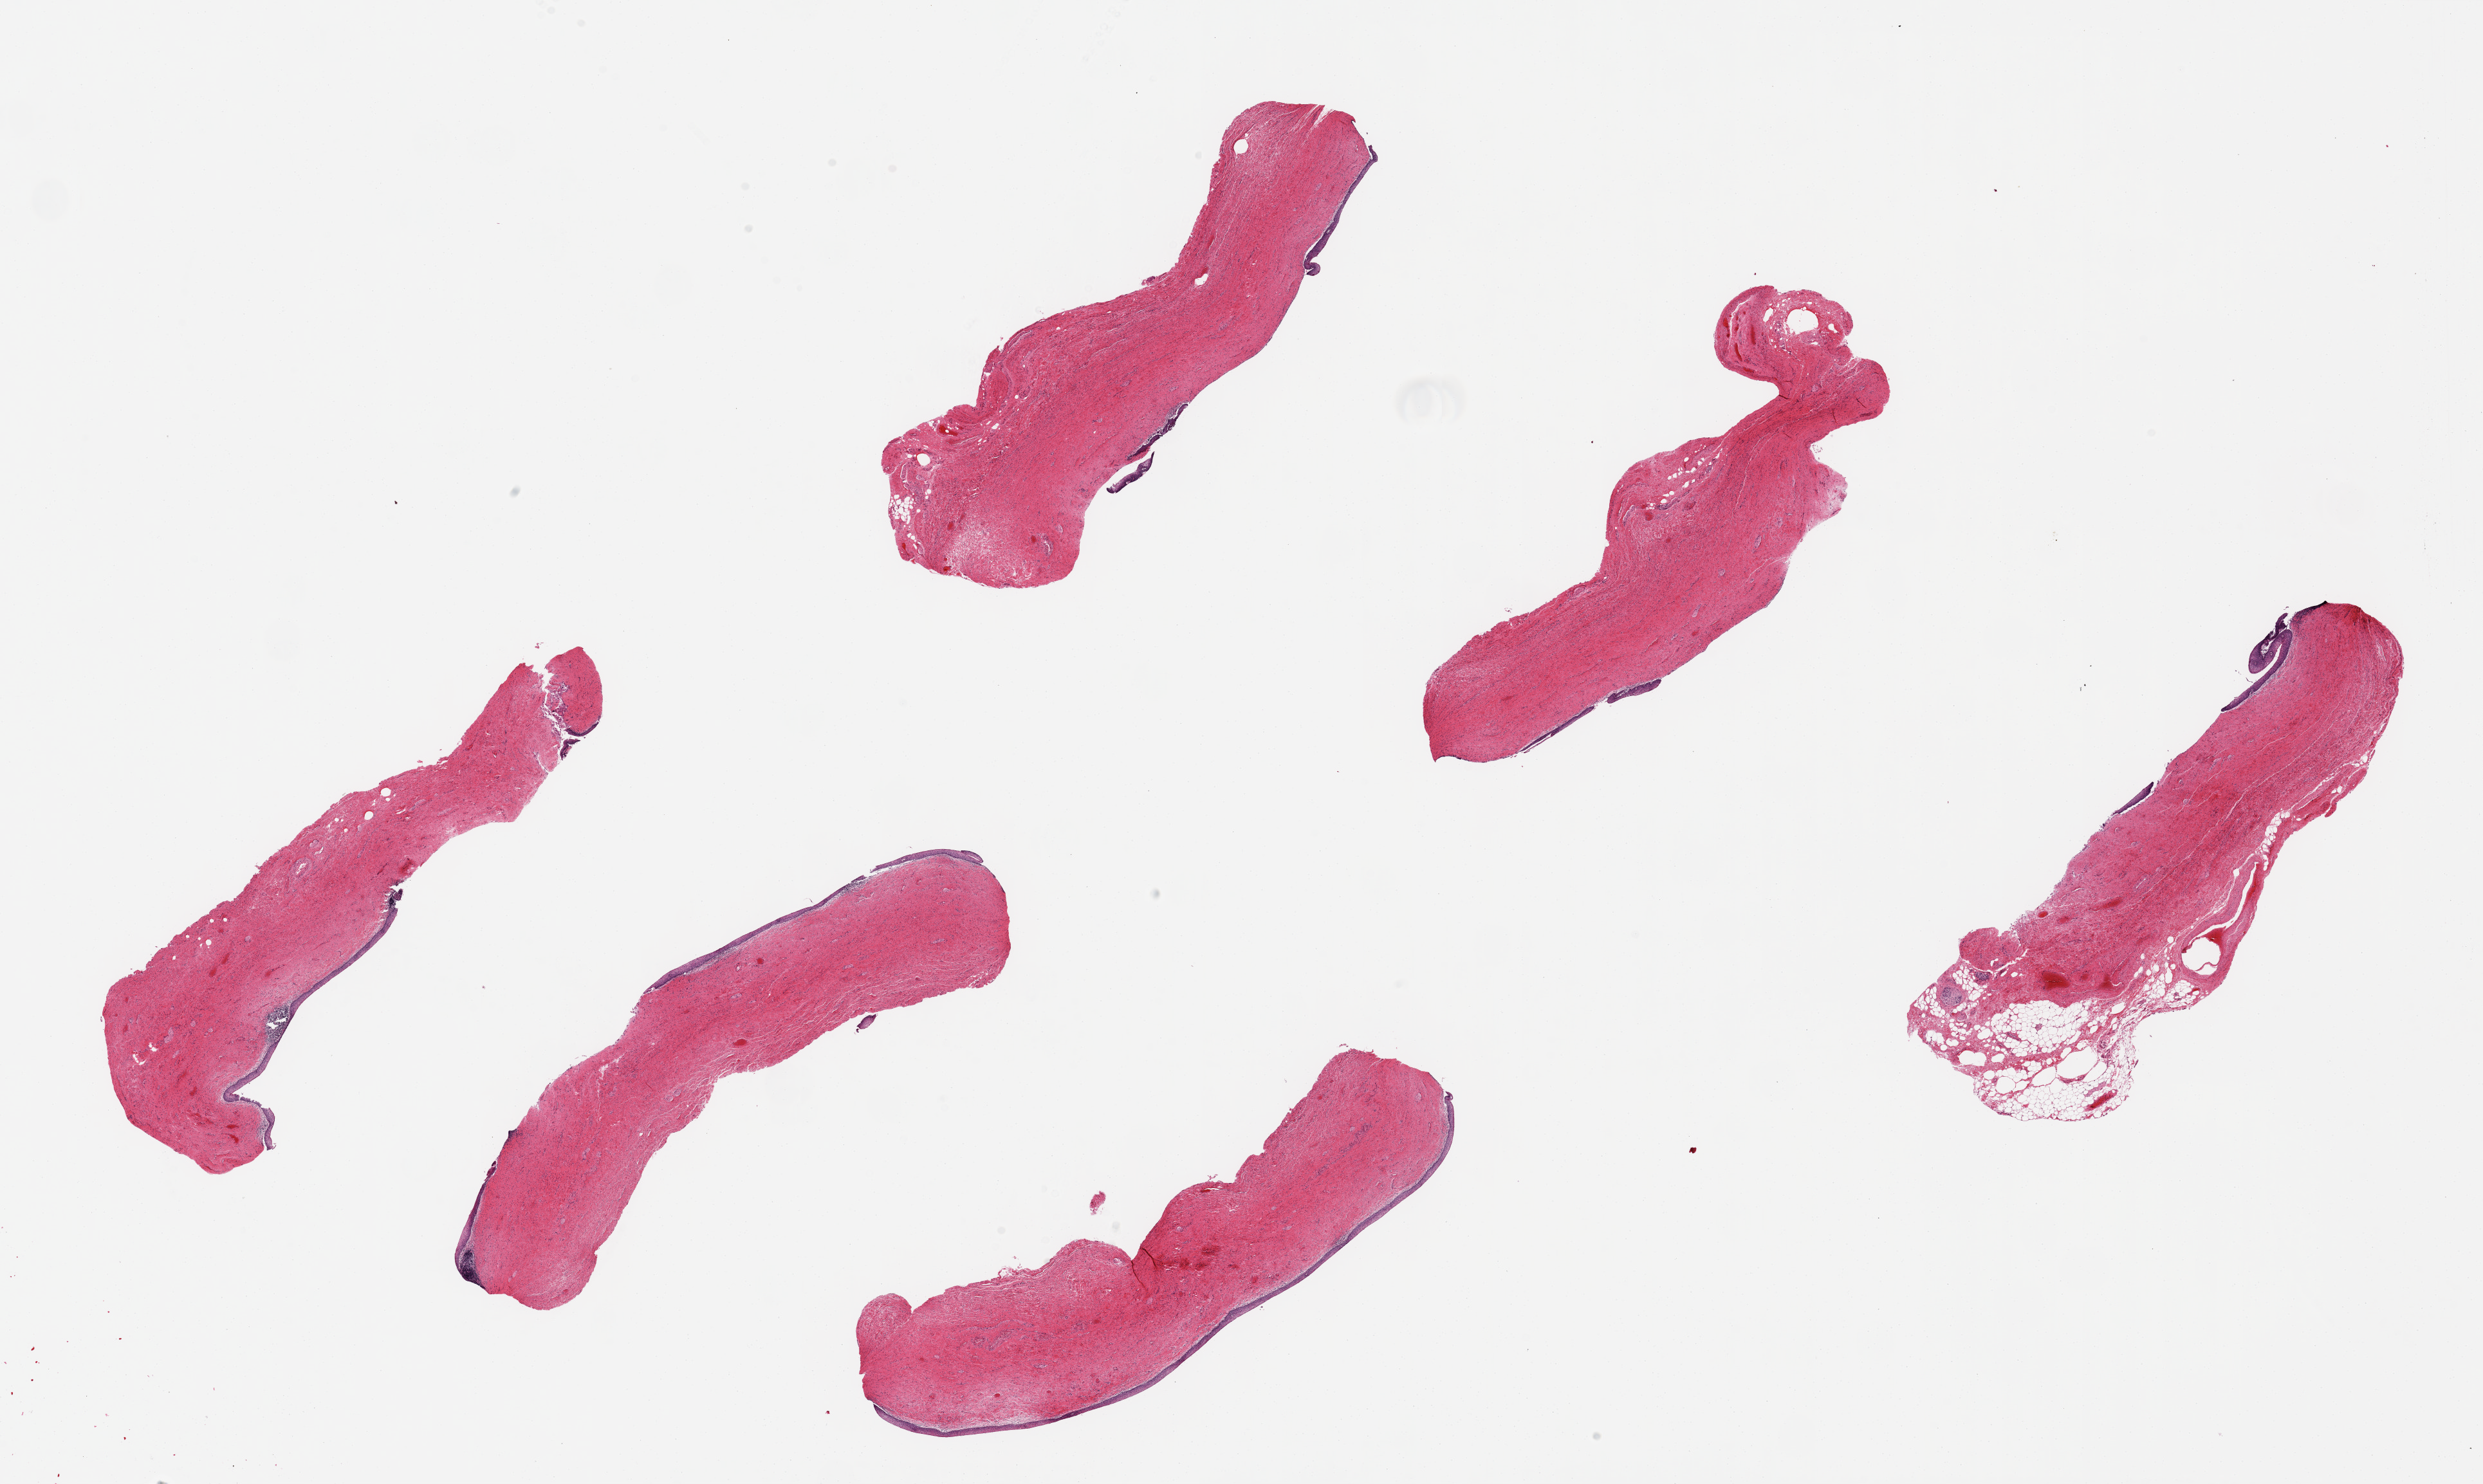
Digitized hematoxylin and eosin (H&E)-stained section, brightfield — low-resolution overview of the scanned area, about 30.5 x 18.2 mm (from a 20x scan), PAXgene-fixed, paraffin-embedded tissue, target tissue: vagina, donor tissue sample.
• reviewer comment on this tissue sample: 6 pieces up to 8x2.5 mm; epithelium partly sloughed; chronic inflammation